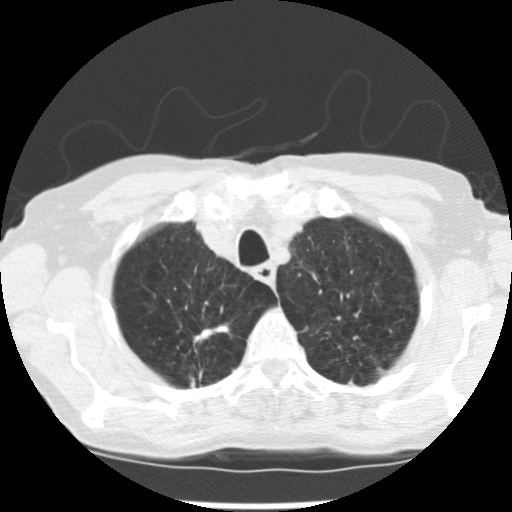
Low-dose screening chest CT, axial slice, first (baseline) screen, lung window (W 1500 / L -600 HU), standard (soft-tissue) reconstruction kernel (STANDARD), slice 35 of 265 in the series, 512 × 512 image matrix. Female, age 72 years at enrolment. Current smoker at enrolment.
- Expert-annotated lung lesion, box from (x=180, y=312) to (x=232, y=352) px.
- The screening reader recorded 3 non-calcified nodules or masses ≥4 mm on this exam (right upper lobe, left upper lobe, left lower lobe); which of them this box marks is not recorded.
- Official screen result: positive, change unspecified: nodule(s) >= 4 mm or enlarging nodule(s), mass(es), or other non-specific abnormalities suspicious for lung cancer.
- Lung cancer was diagnosed 50 days after this screen: adenocarcinoma, NOS, right upper lobe, moderately differentiated (G2), stage IB (AJCC 6th edition), 22 mm at pathology.